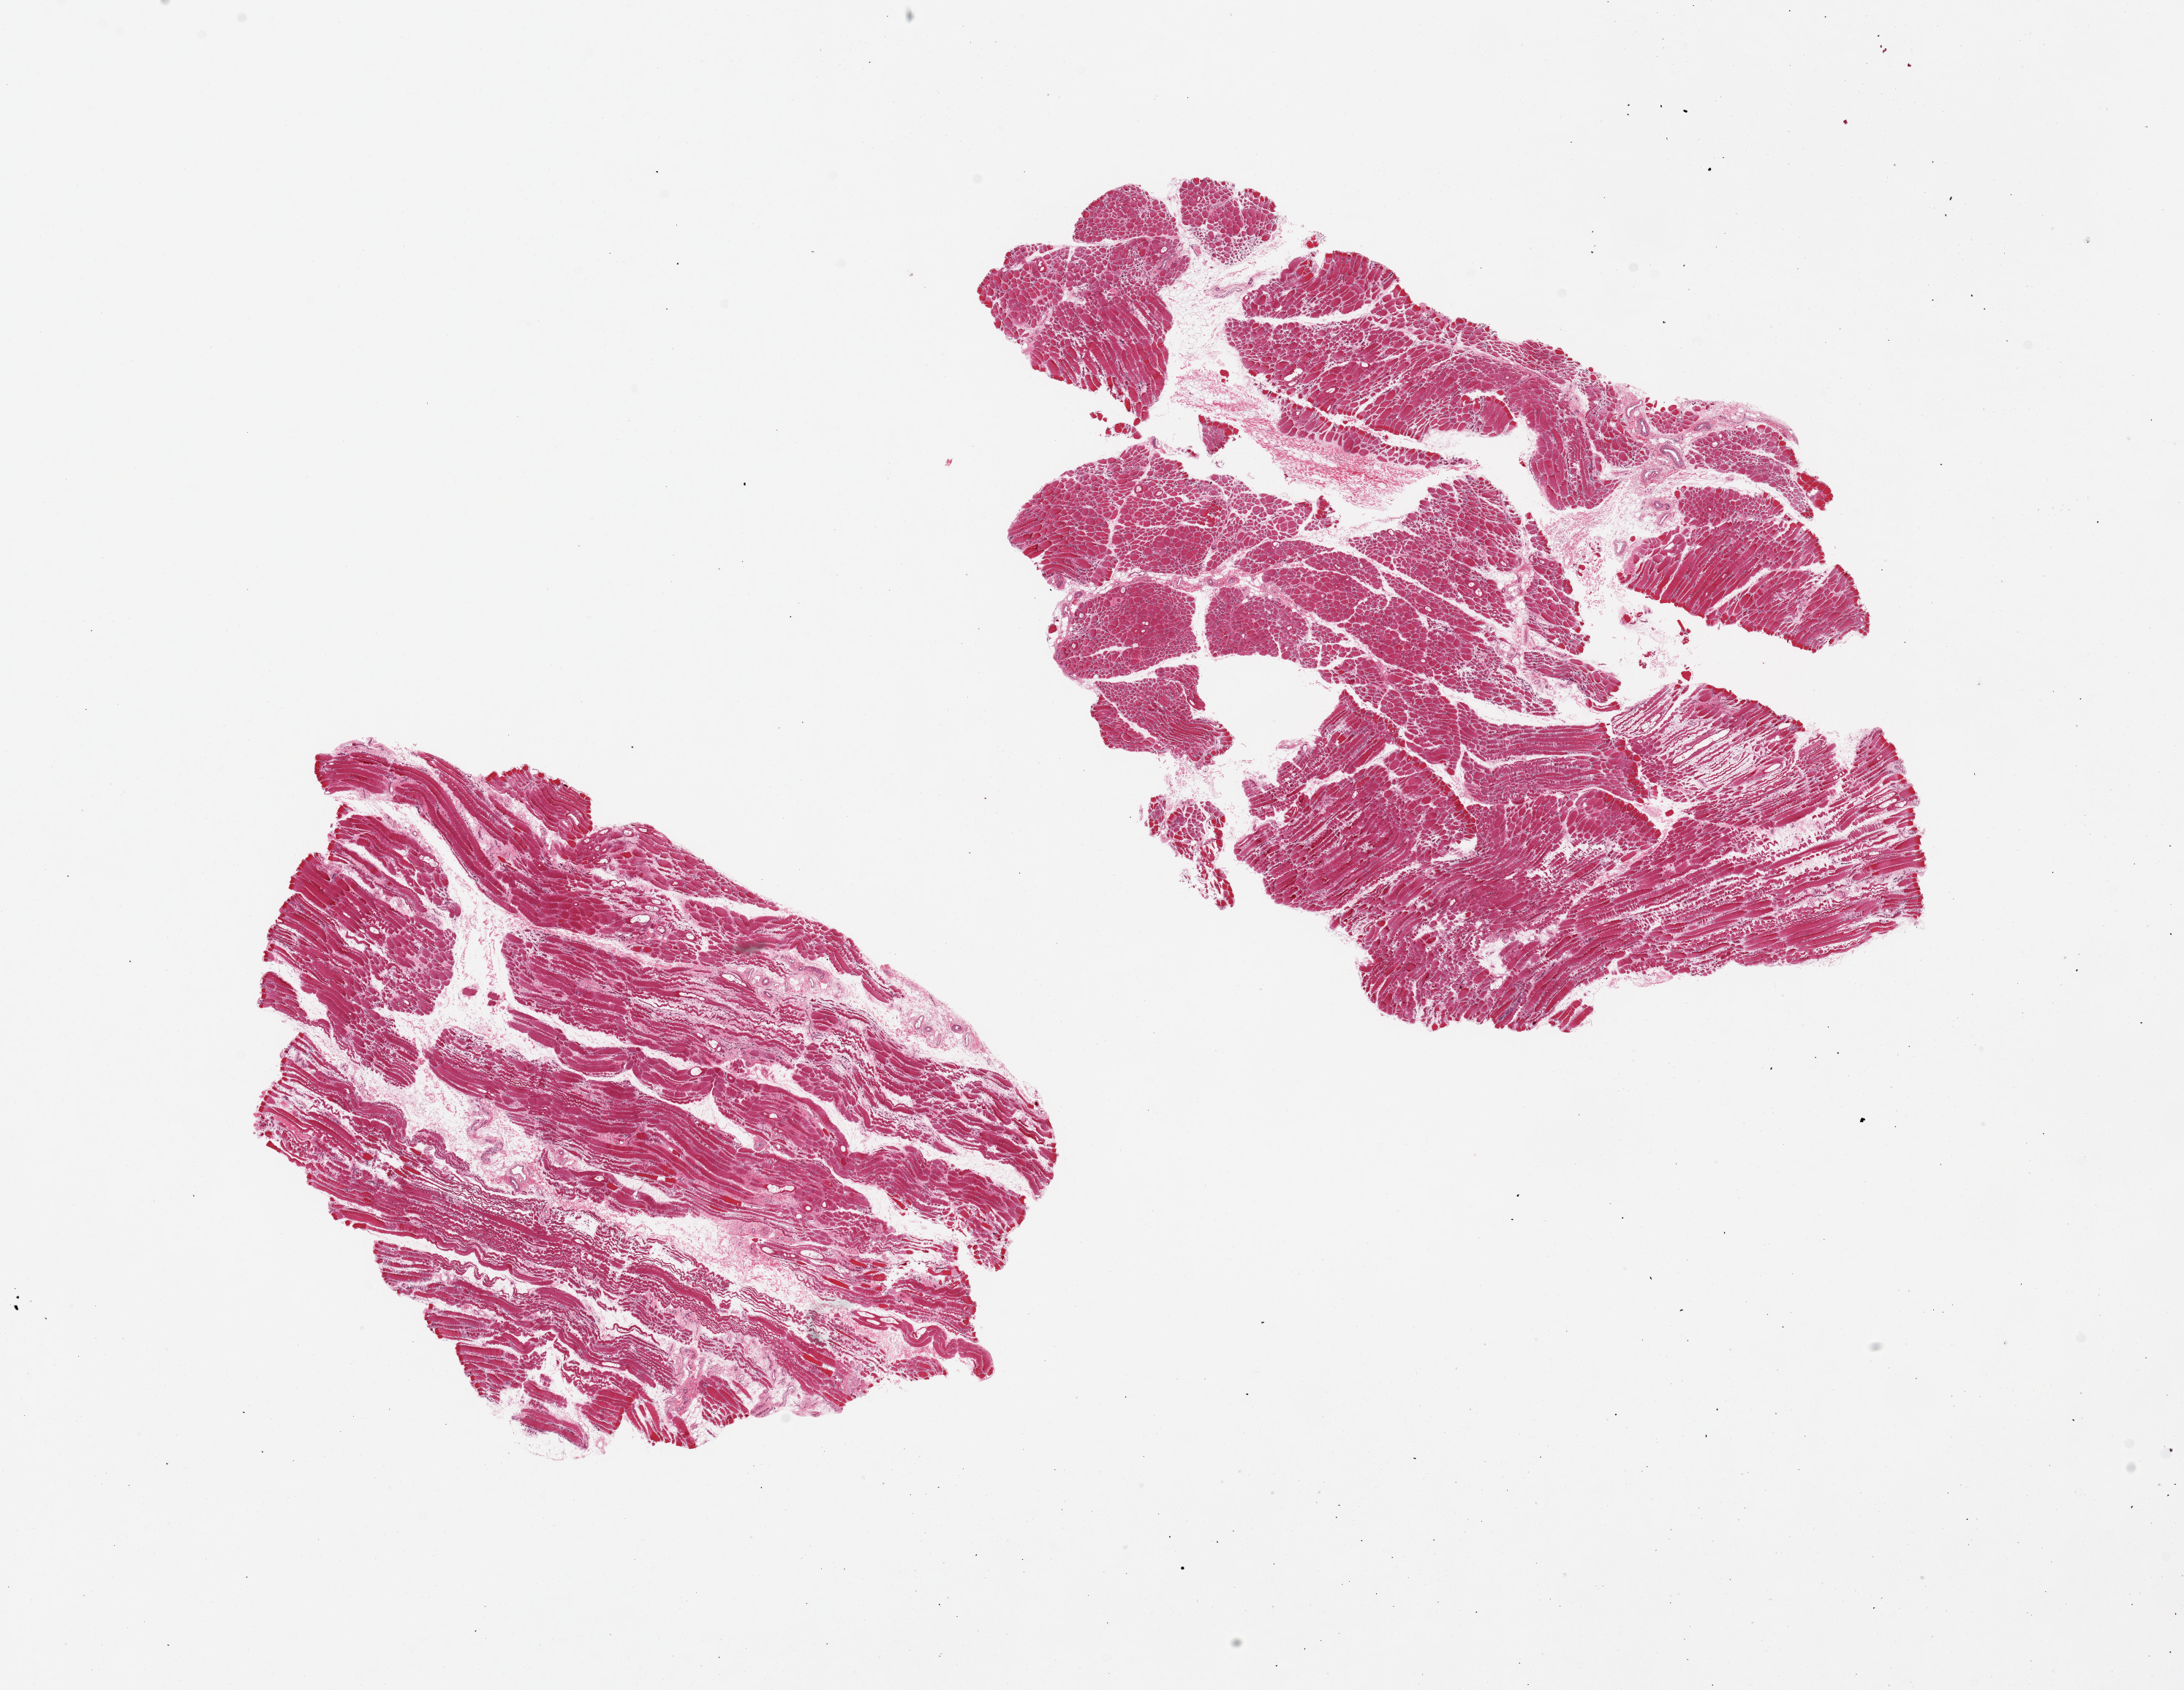
Haematoxylin and eosin whole-slide image, whole scanned area (about 23.6 x 18.3 mm, slide scanned at 20x) shown as a low-resolution overview. PAXgene-fixed paraffin-embedded (PFPE) section. Section of skeletal muscle (target tissue). Donor tissue sample. Male donor.
* reviewer comment on this tissue sample: 2 pieces, 10x7 & 12x8mm; muscle fibers atrophied, interstitial fibrosis